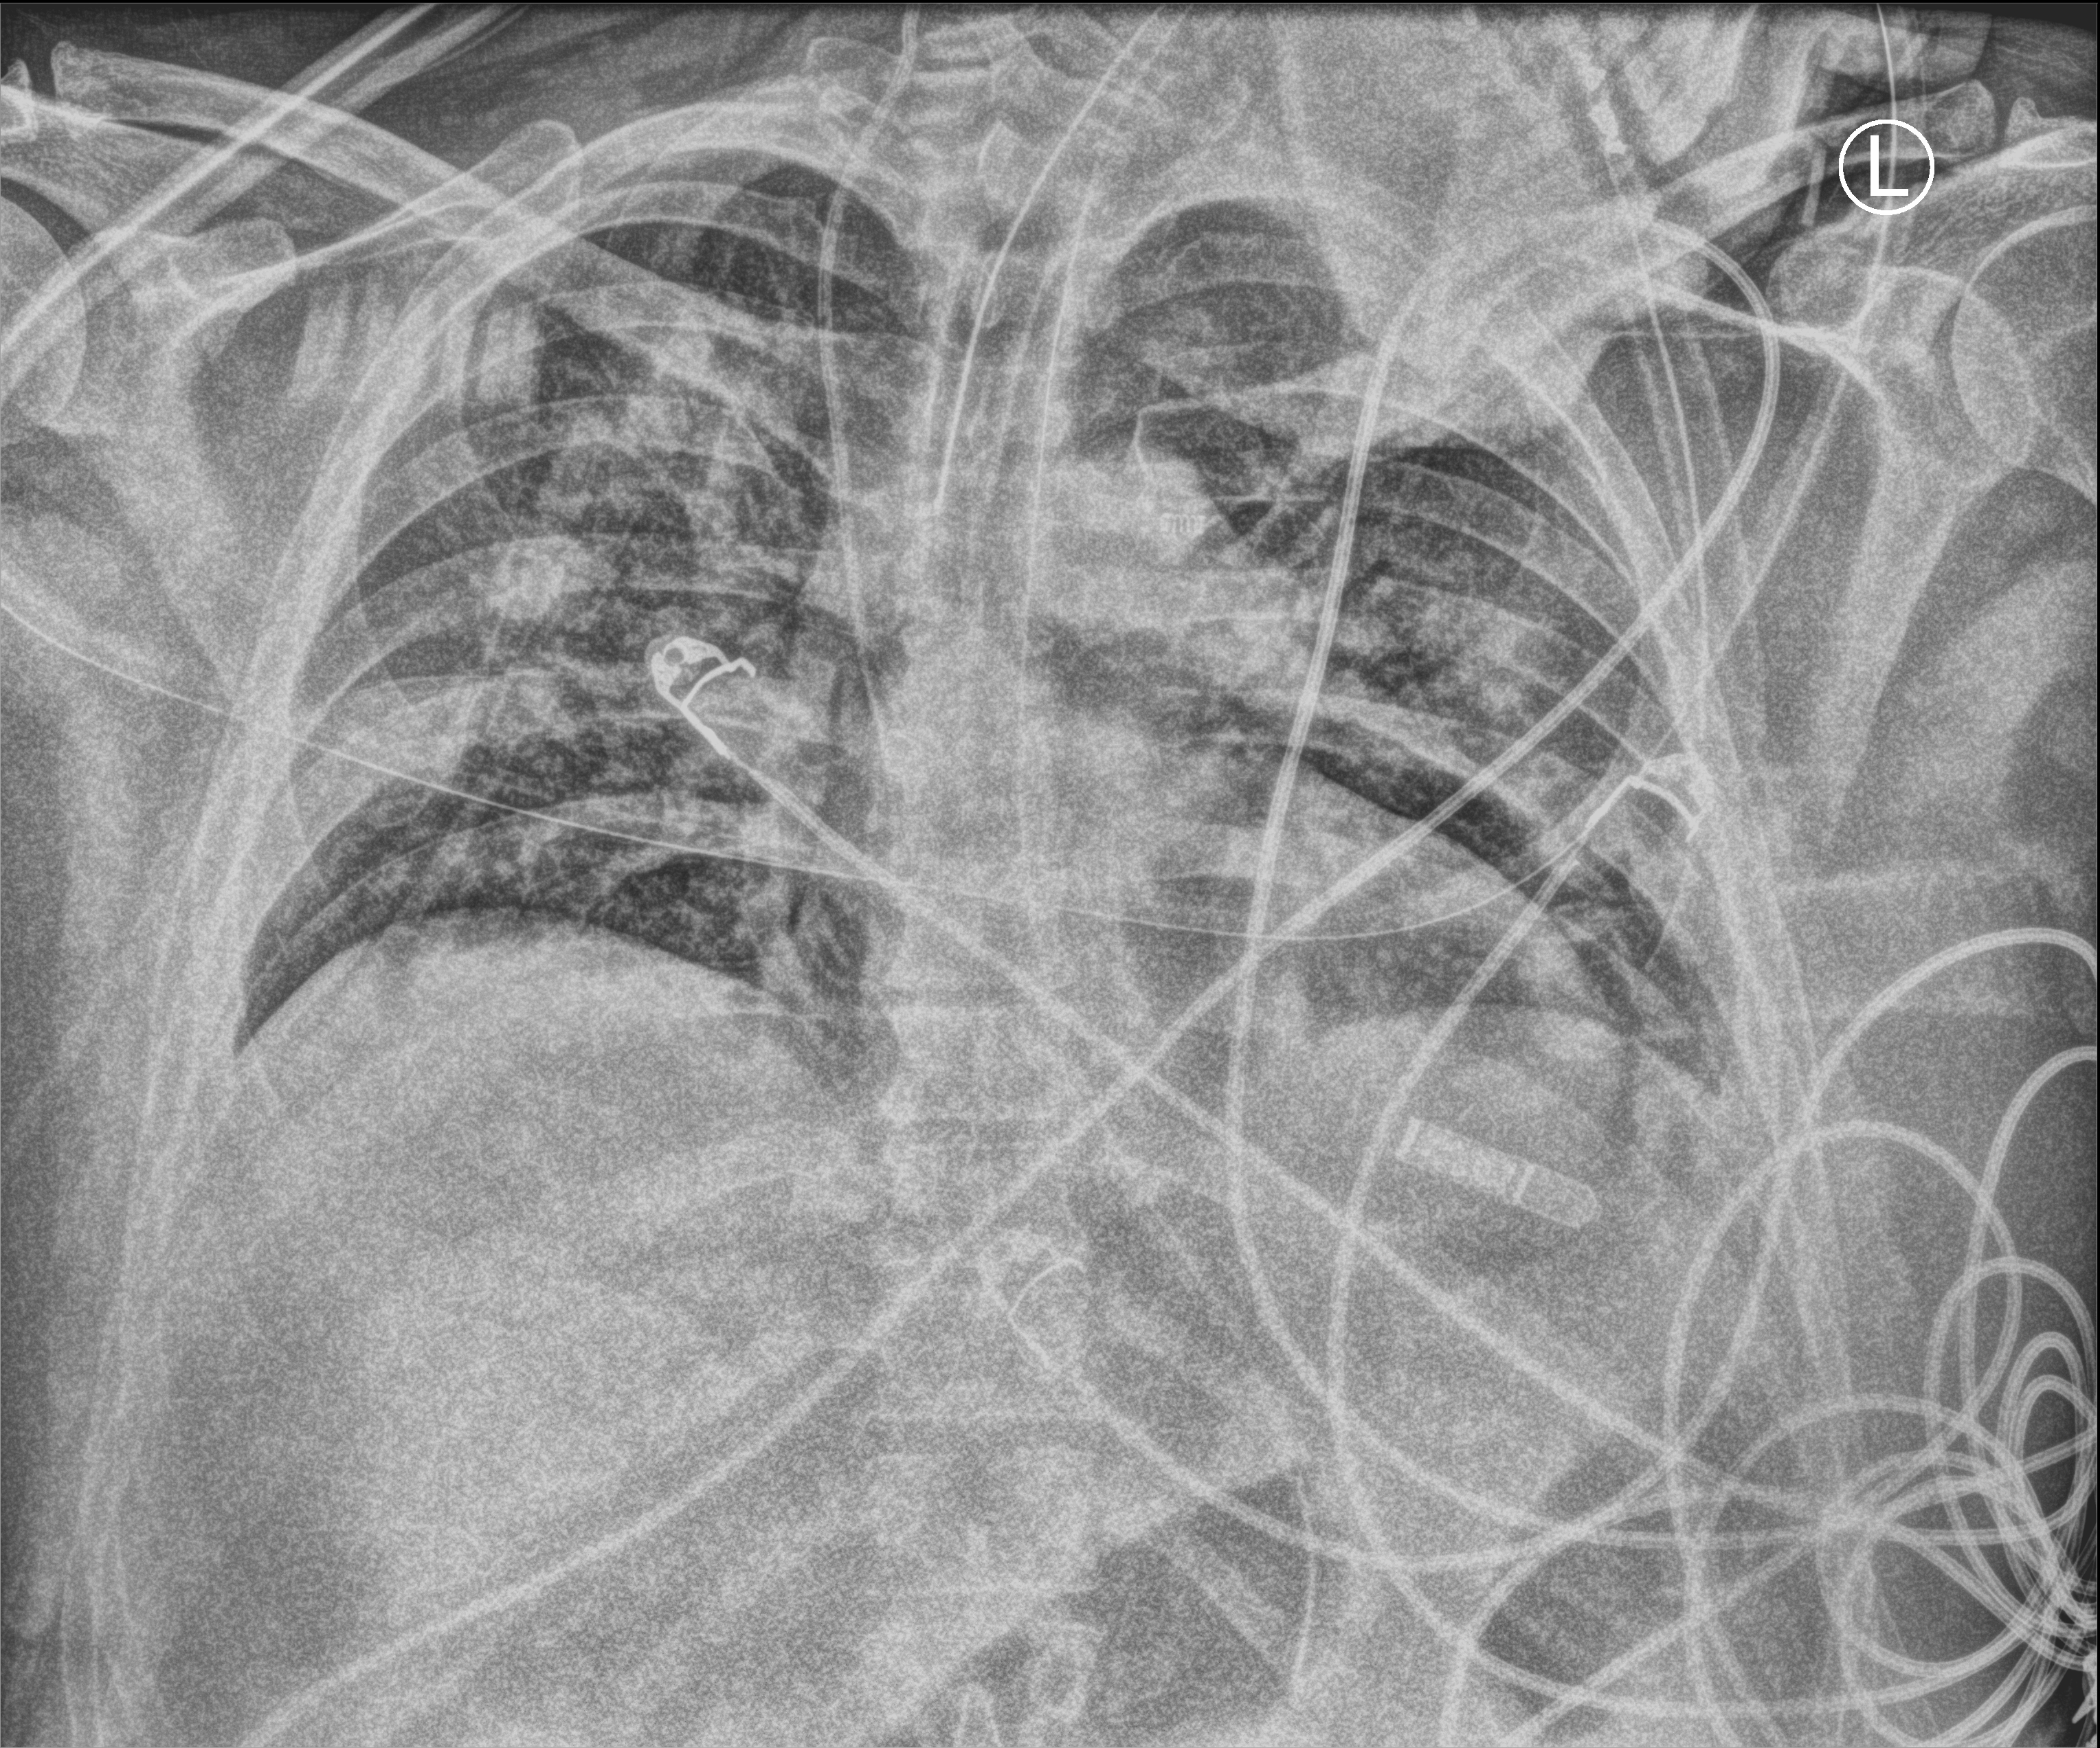
Portable chest radiograph; anteroposterior (AP) projection. Male patient hospitalised with COVID-19, age 18–59 years.
Hospital-stay facts (about this admission, not read from this image; timing relative to this image not recorded): admitted to intensive care during this hospital stay: yes.